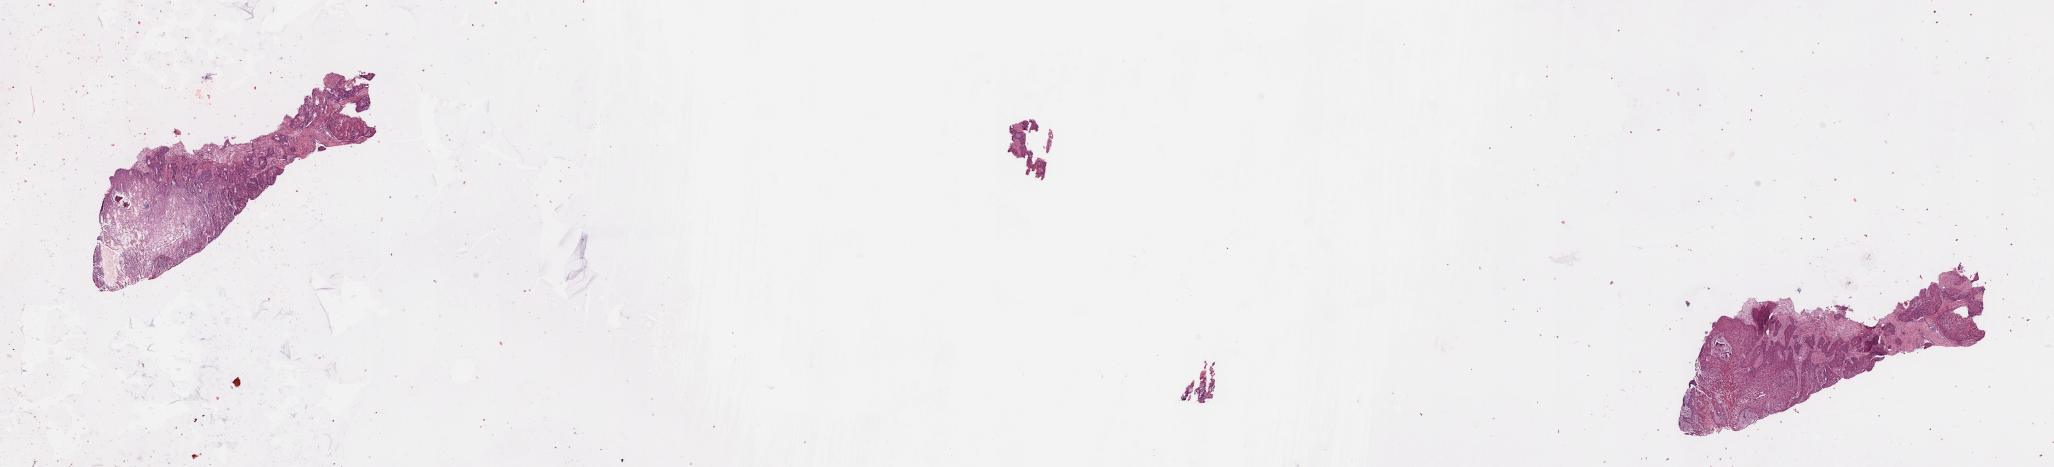
H&E whole-slide image, a low-resolution overview of the entire scanned area, about 32.5 x 7.4 mm. Tumour tissue sample, sampled site: larynx. Male, 64 y/o. Histologic grade: G2 (moderately differentiated). Composition of this section per pathologist review: tumour nuclei 80%, necrosis 10%.
AJCC pathologic stage: IVA. Histologic diagnosis: Squamous cell carcinoma, NOS (larynx, NOS). Primary tumour site (as recorded): larynx.